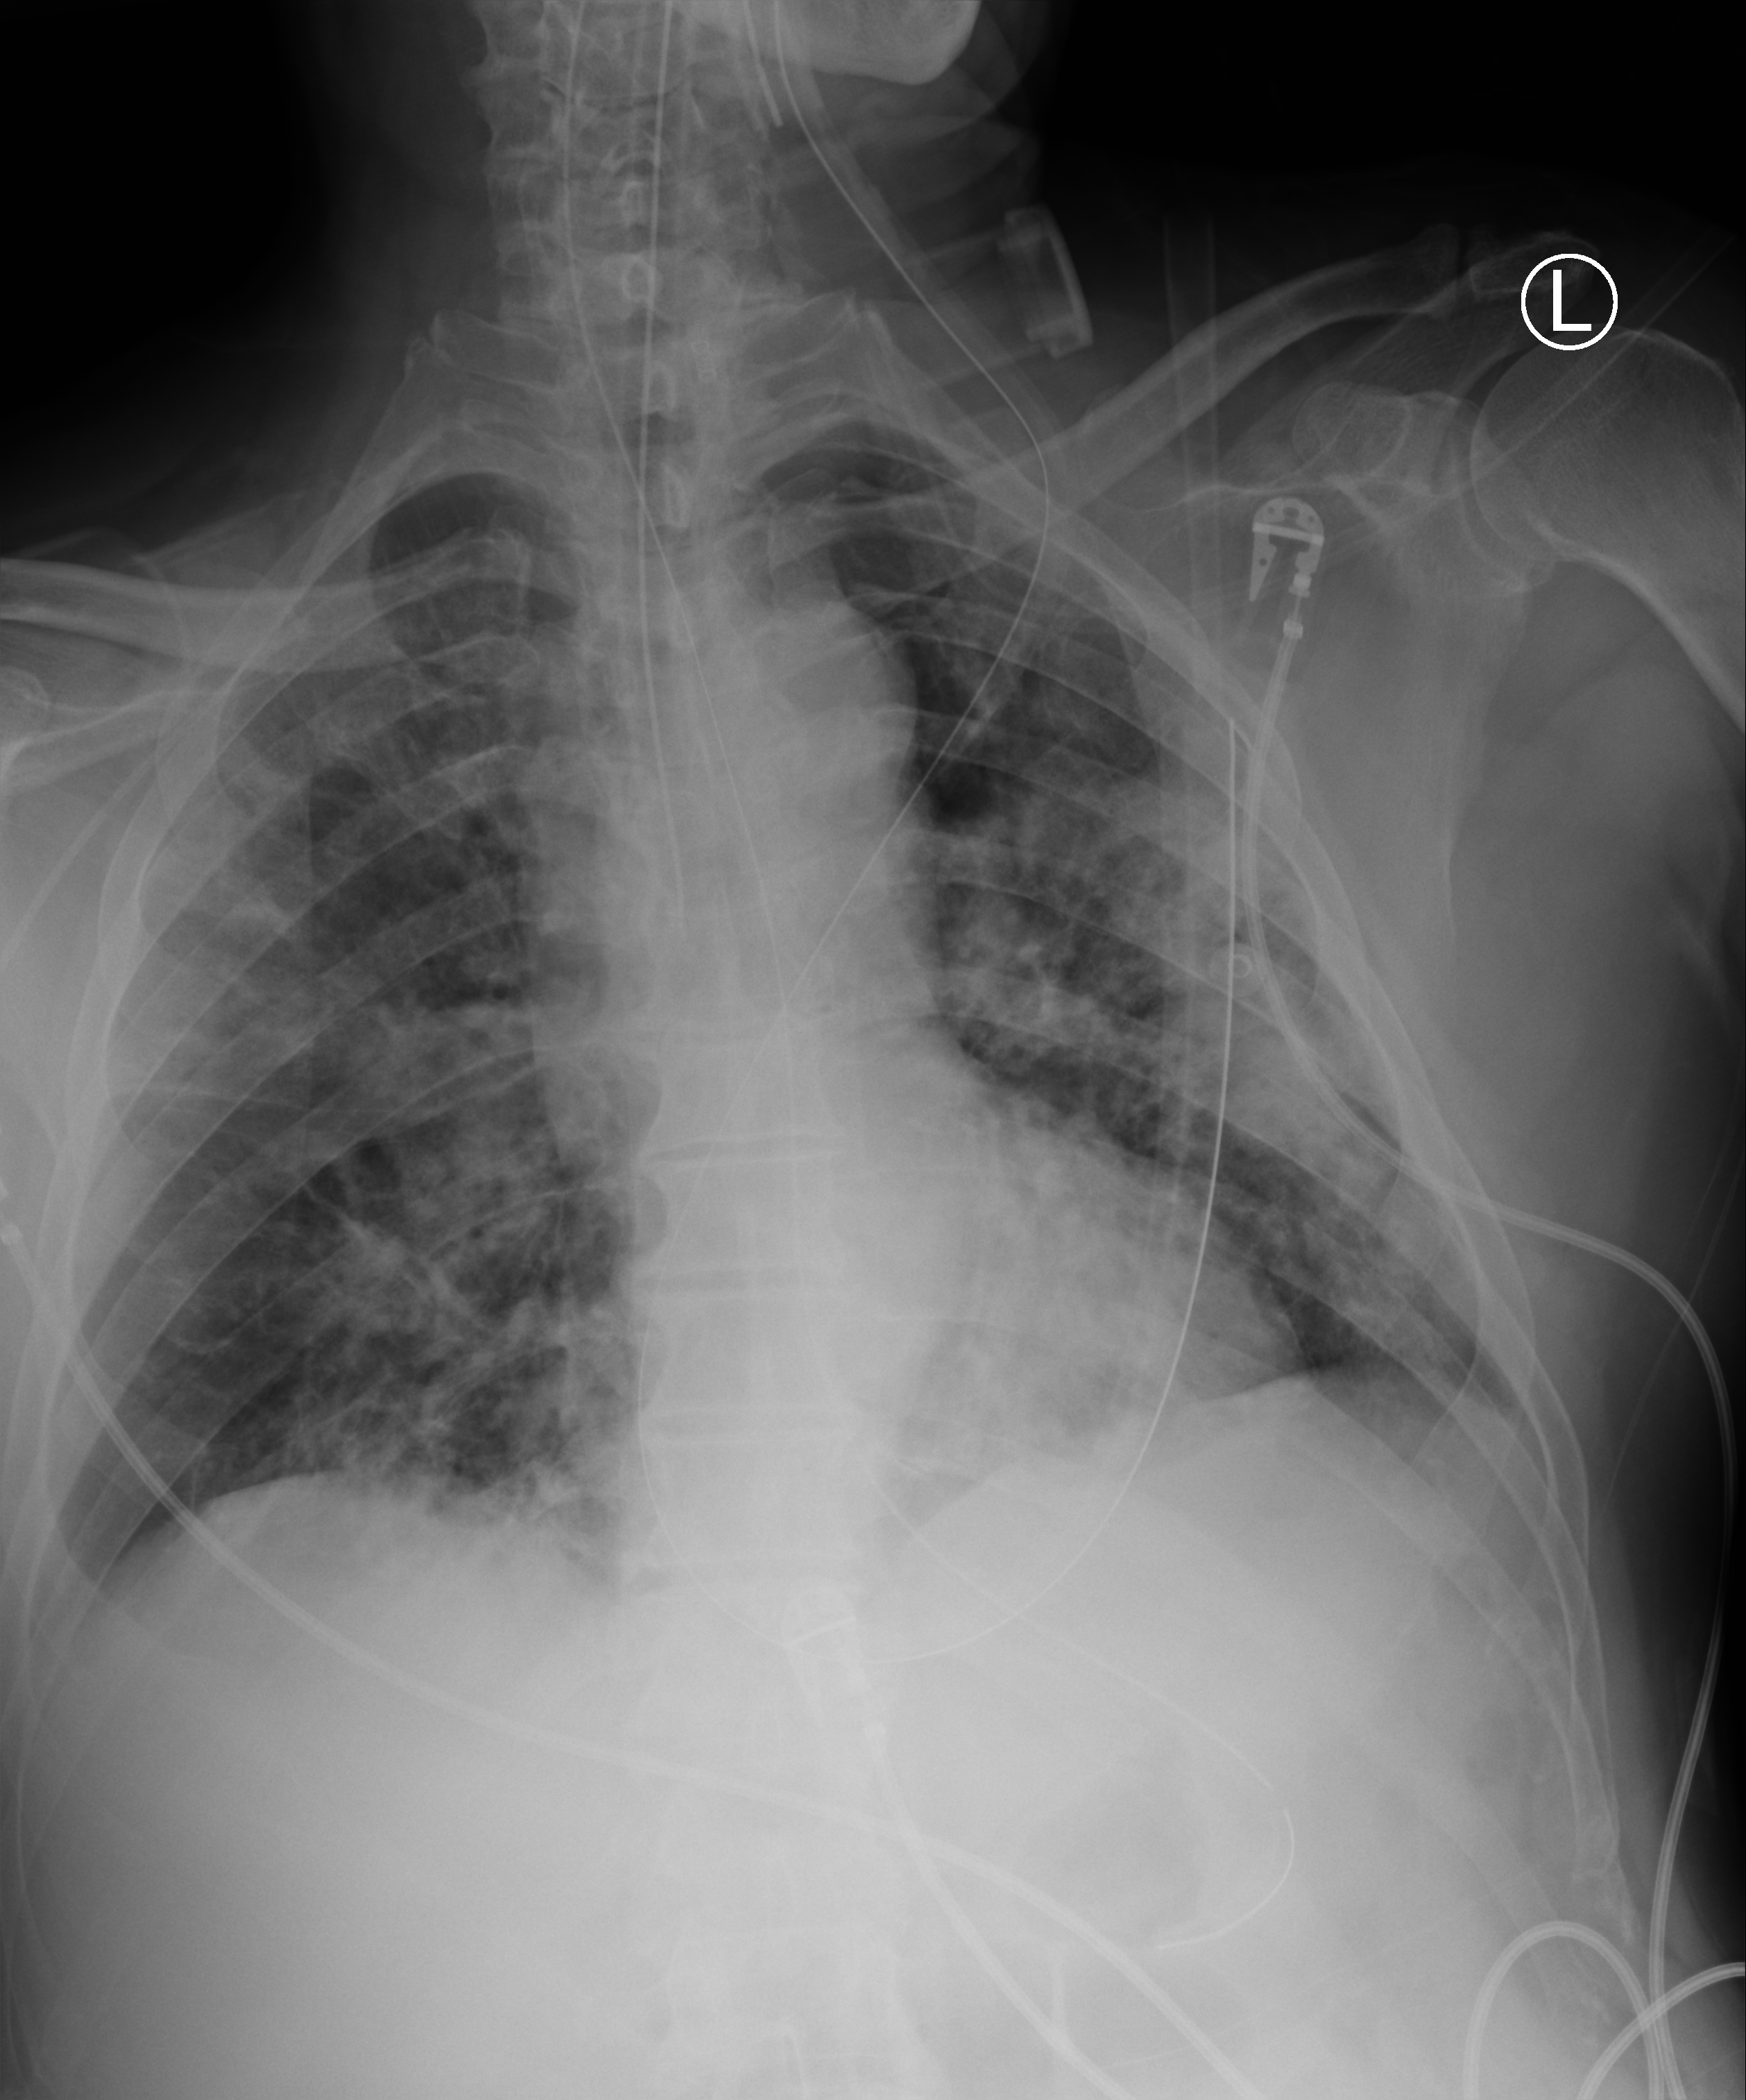
Bedside chest radiograph (computed radiography); anteroposterior (AP) projection. Patient hospitalised with COVID-19; male, aged 60–74 years.
From the hospital-stay record, not from the radiograph (when in the stay this image was taken is not recorded): mechanically ventilated during this hospital stay: yes; admitted to intensive care during this hospital stay: yes.